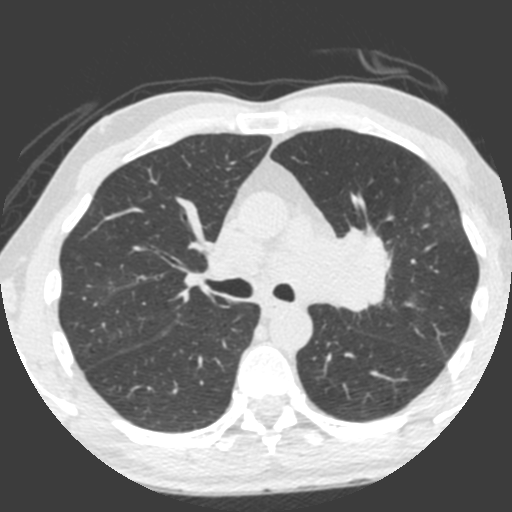
Low-dose screening chest CT, one axial slice; position 139 of 212 along the scan axis; lung window (W 1500 / L -600 HU); 512 × 512 image matrix, field of view 315 × 315 mm.
Annotated regions visible in this slice (outlined manually by an expert reader):
- lesion 1 (tumor, upper lobe of left lung): box from (x=321, y=228) to (x=391, y=312) px